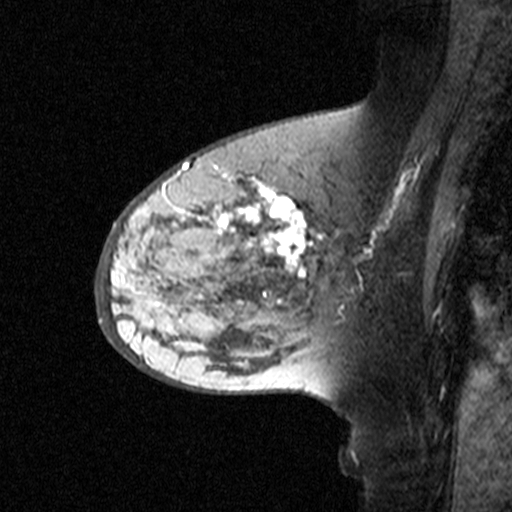
Breast MRI (dynamic contrast-enhanced), one sagittal slice. Slice 25 of 44 in the series (ordered by position). Dynamic contrast-enhanced study with each time point stored as its own series, time point 2 of 3 at this slice position (early post-contrast, ordered by acquisition time). 1.5 T. TE 4.5 ms, TR 11 ms. 3 mm slice thickness. 512 × 512 image matrix. Patient: female, 65 years. From the clinical record (not read from this slice): setting: breast cancer imaged before/during neoadjuvant chemotherapy; receptor status: HER2-positive.
Annotated regions visible in this slice (semi-automatic segmentation, software-assisted and operator-edited):
- analysis volume of interest (the breast-tissue region the enhancement analysis was run in; not a lesion): bounding box (x1, y1, x2, y2) in pixels: (160, 172, 329, 345)
- tumour enhancement mask (voxels above the 90 % enhancement threshold inside the analysis volume of interest): (173, 175, 316, 308)